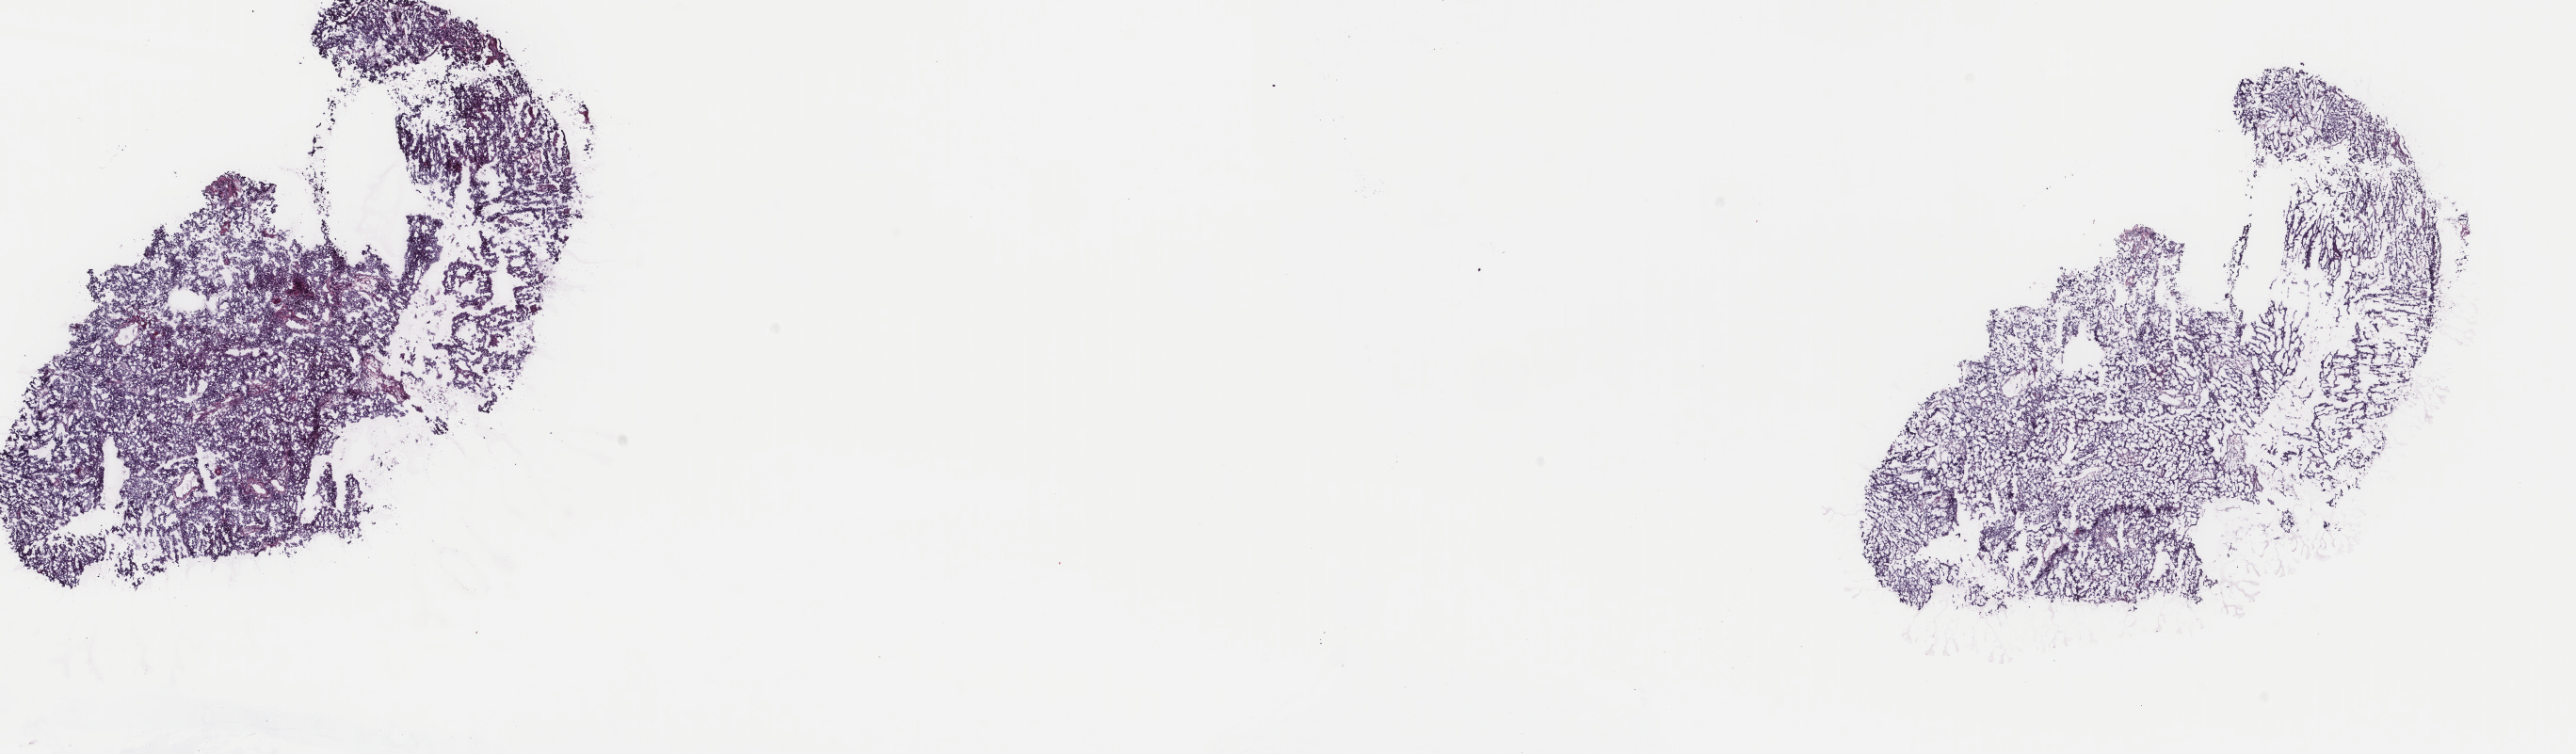
Whole-slide histology image, Hematoxylin and eosin (H&E) stained — shown as a low-resolution overview of the whole scanned area (about 21.7 x 6.4 mm, slide scanned at 40x). Frozen section. Primary tumour sample from the bladder. Male patient; age at initial diagnosis 73 years.
Pathologic diagnosis: Papillary transitional cell carcinoma.